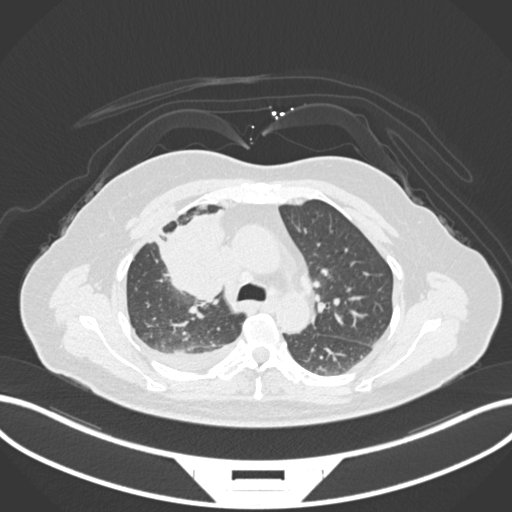
Chest CT, one axial slice. Slice 104 of 172 in the series (ordered by position). 120 kVp. Lung window (W 1500 / L -600 HU). 1 mm slice thickness. 512 × 512 image matrix, field of view 400 × 400 mm. Patient: female, 52 years. Case-level facts recorded for this patient, not image findings: clinical TNM (as recorded): T3 N1 M1.
Structures marked on this image (bounding box drawn by a radiologist):
- lung tumour (recorded histology: adenocarcinoma): box from (x=152, y=209) to (x=226, y=300) px